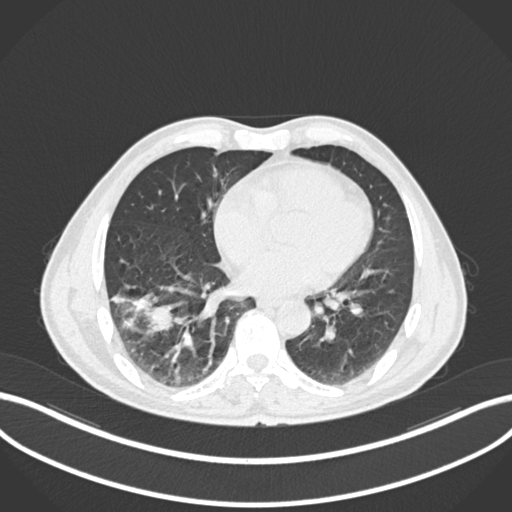
Chest CT, one axial slice; slice 67 of 208 in the series (ordered by position); reconstruction kernel B30f; lung window (W 1500 / L -600 HU); 1 mm slice thickness; 512 × 512 image matrix, field of view 400 × 400 mm. Patient: male, 58 years. Case-level facts recorded for this patient, not image findings: clinical TNM (as recorded): T3 N0 M0; histopathological grade: G2.
Outlined on this slice (rectangle marked by the reading radiologist):
- lung tumour (recorded histology: squamous cell carcinoma): box from (x=112, y=289) to (x=177, y=339) px